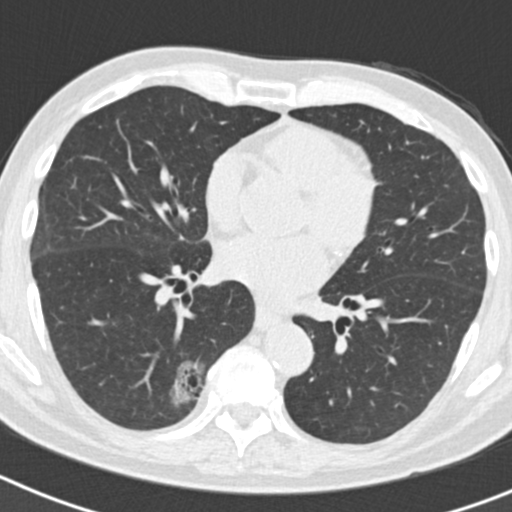
Axial slice from a low-dose chest CT screening exam; second screening round (one year after baseline); lung window (W 1500 / L -600 HU); 2 mm slice thickness; standard (soft-tissue) reconstruction kernel (B30f). Male, age 70 years at enrolment. Current smoker at enrolment.
Expert-annotated lung lesion, bounding box [x1, y1, x2, y2] px = [126, 361, 207, 431]. The screening reader recorded 5 non-calcified nodules or masses ≥4 mm on this exam (right lower lobe, right lower lobe, right upper lobe, right upper lobe, left upper lobe); which of them this box marks is not recorded. Official screen result: positive, other.